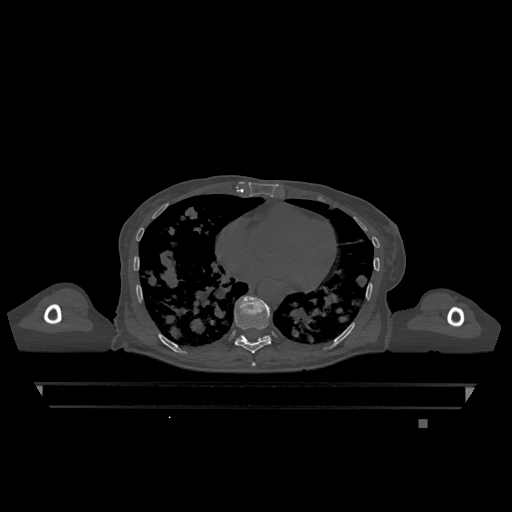
CT including the spine, one axial slice. Slice 683 of 1317 in the series (ordered by position). Bone window (W 1800 / L 400 HU). 512 × 512 image matrix. Patient: female, 74 years. From the clinical record (not read from this slice): primary cancer: lung; vertebrae with lytic lesions (as recorded): T1, T4, T5, T6, L4, L5.
Annotated regions visible in this slice (semi-automatic segmentation, software-assisted and operator-edited):
- T10 vertebra: bounding box <237,335,270,340> (left, top, right, bottom; pixels)
- T7 vertebra: <252,362,256,366>
- T9 vertebra: <234,296,271,354>